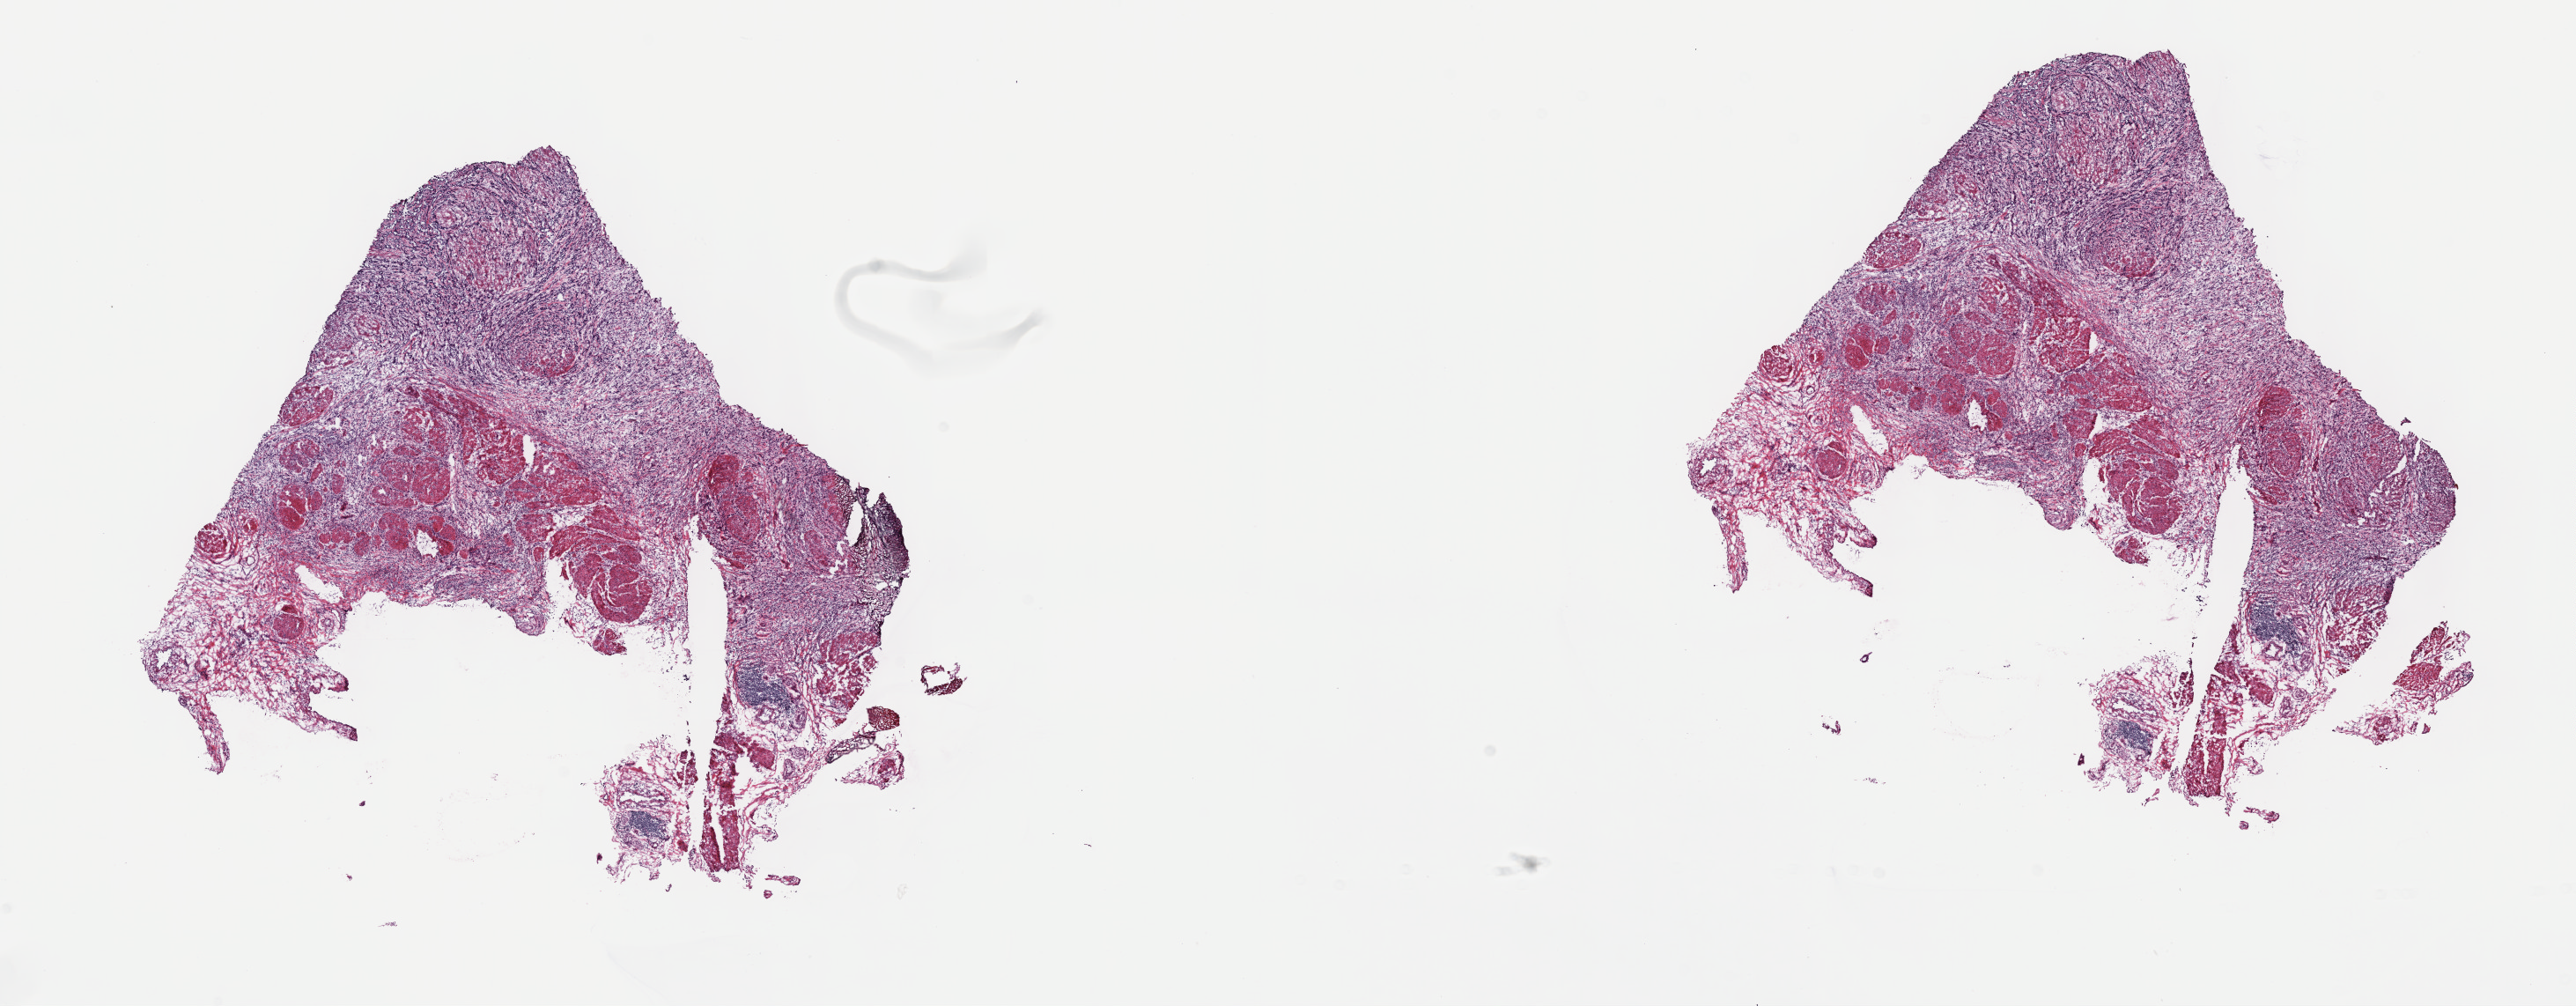
Whole-slide histology image, Hematoxylin and eosin (H&E) stained — a low-resolution overview of the entire scanned area, about 23.7 x 9.2 mm. Frozen section. Primary tumour sample from the bladder. Patient: female, age at initial diagnosis 77 years. Histologic grade: high grade. Pathologist review of this section (percent, as recorded): tumour cells 45%, tumour nuclei 70%, normal cells 0%, stromal cells 50%, necrosis 5%. Inflammatory infiltration, as recorded: lymphocyte infiltration 22%, monocyte infiltration 2%, neutrophil infiltration 2%.
TNM: T3b N0 MX. AJCC pathologic stage: III (6th edition). Pathologic diagnosis: Transitional cell carcinoma.